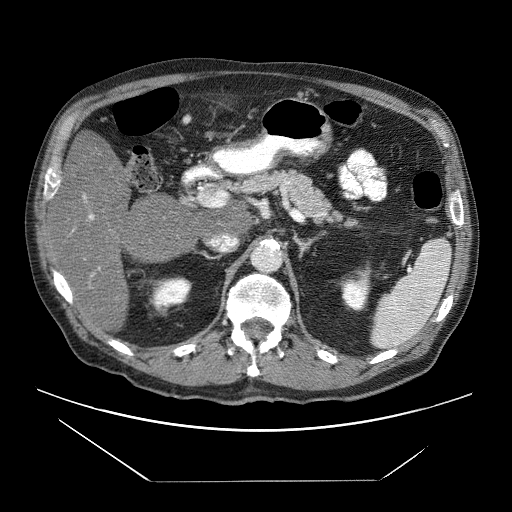
Contrast-enhanced abdominal CT (liver protocol), one axial slice; position 30 of 83 along the scan axis; reconstruction kernel STANDARD; soft-tissue window (W 400 / L 40 HU); 2.5 mm slice thickness; 512 × 512 image matrix. Case-level facts recorded for this patient, not image findings: diagnosis: hepatocellular carcinoma (patient treated with transarterial chemoembolisation; whether this scan precedes or follows treatment is not stated here); TNM stage (as recorded): Stage-IVB; Child-Pugh class: B.
Outlined on this slice (semi-automatically segmented with operator editing):
- liver parenchyma outside the tumour (the mass and vessels are separate outlines, so this box may not span the whole liver): bounding box [x1, y1, x2, y2] px = [52, 146, 251, 328]
- liver vessels: [84, 196, 94, 276]